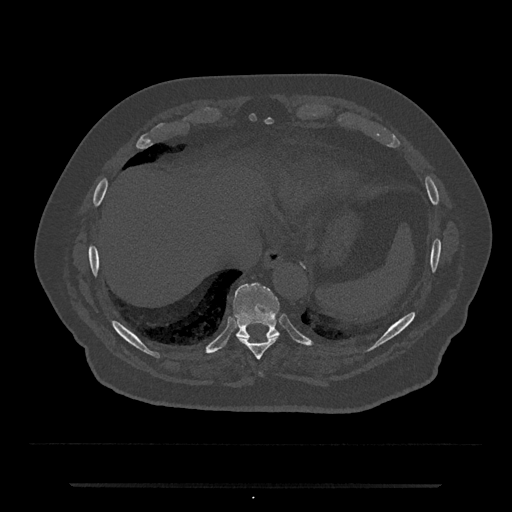
CT including the spine, one axial slice; slice 735 of 797 in the series (ordered by position); bone window (W 1800 / L 400 HU); 0.5 mm slice thickness; 512 × 512 image matrix, field of view 434 × 434 mm. Patient: male, 80 years. From the clinical record (not read from this slice): primary cancer: prostate; vertebrae with lytic lesions (as recorded): L1, T11.
Structures marked on this image (semi-automatic segmentation, software-assisted and operator-edited):
- T10 vertebra: bounding box (x1, y1, x2, y2) in pixels: (233, 283, 280, 338)
- T9 vertebra: (237, 336, 278, 360)